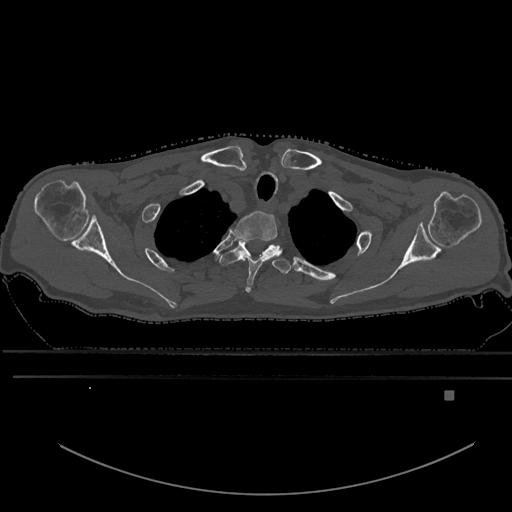
CT including the spine, one axial slice. Slice 514 of 969 in the series (ordered by position). Bone window (W 1800 / L 400 HU). 0.5 mm slice thickness. 512 × 512 image matrix, field of view 456 × 456 mm. Patient: male, 82 years. Case-level facts recorded for this patient, not image findings: primary cancer: prostate; vertebrae with lytic lesions (as recorded): T11, T9, T8, T2.
Structures marked on this image (semi-automatic segmentation, software-assisted and operator-edited):
- T1 vertebra: bounding box [x1, y1, x2, y2] px = [234, 211, 279, 293]
- T2 vertebra: [220, 239, 289, 274]